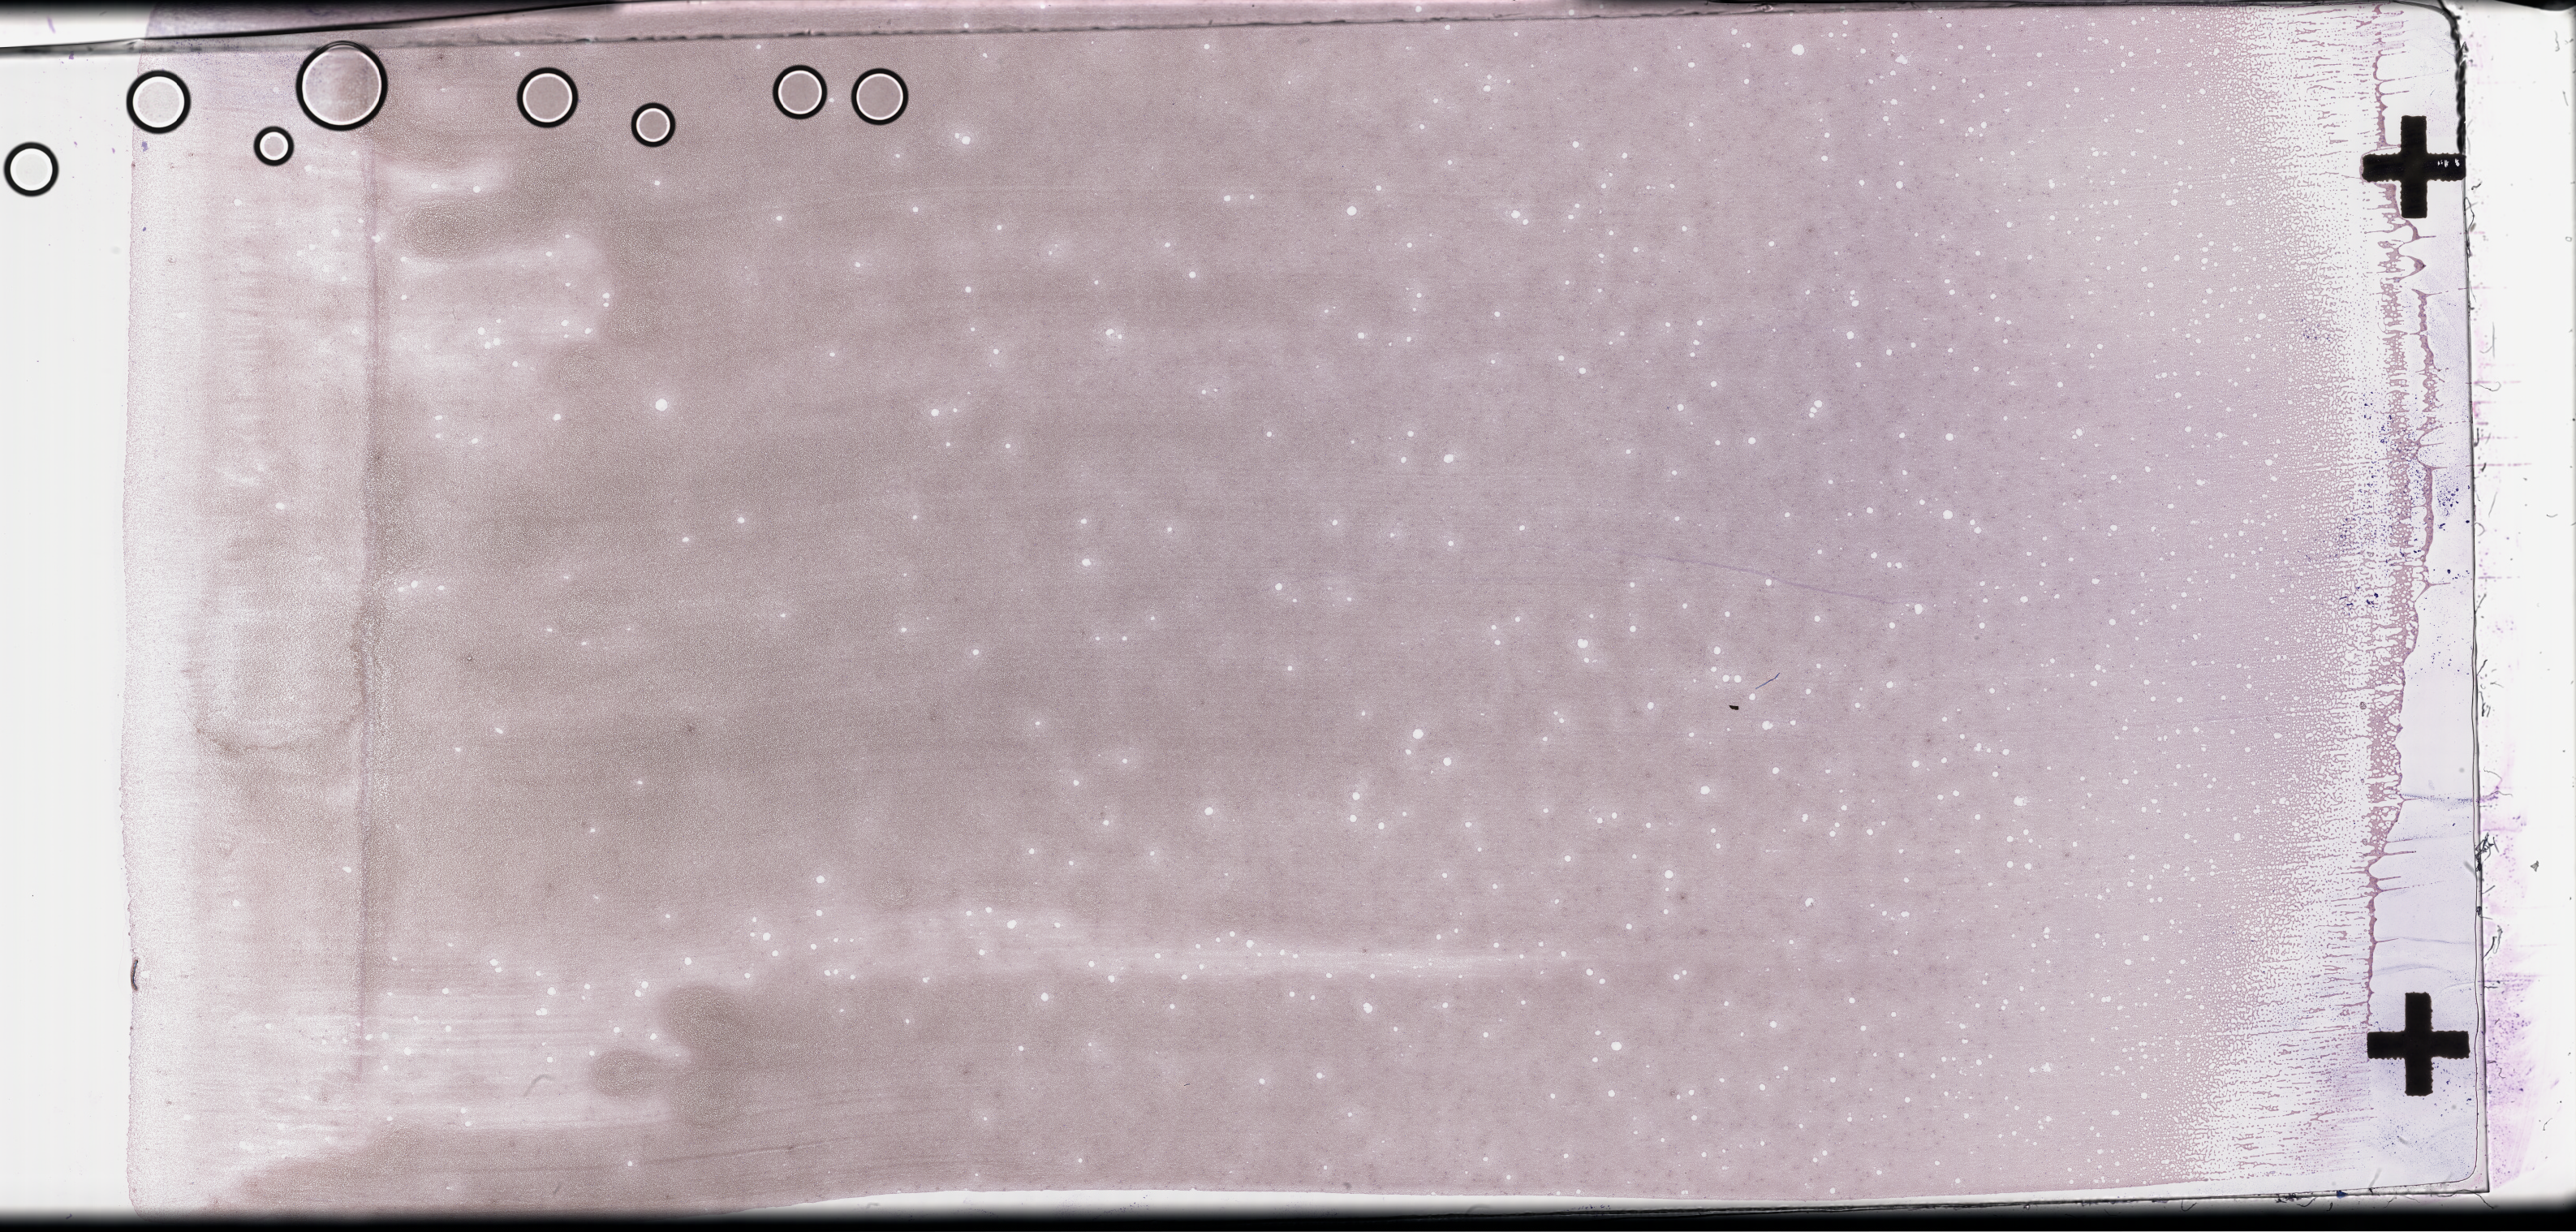
Whole-slide image of a whole blood smear, Wright–Giemsa stain — a low-resolution overview of the entire scanned area, about 51.3 x 24.5 mm; smear from an EDTA sample; specimen time point: collected on treatment. Patient: male.
From a patient with: Plasma Cell Myeloma.